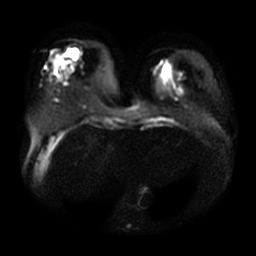
Breast MRI, one axial slice. Slice 9 of 29 in the series (ordered by position). Diffusion-weighted series; image 2 of 4 stored at this slice position (different b-values; order by instance number). 3 T. 256 × 256 image matrix, field of view 380 × 380 mm. Female patient.
Annotated regions visible in this slice (outlined manually by an expert reader):
- tumour on diffusion-weighted imaging: bounding box (x1, y1, x2, y2) in pixels: (65, 51, 68, 56)